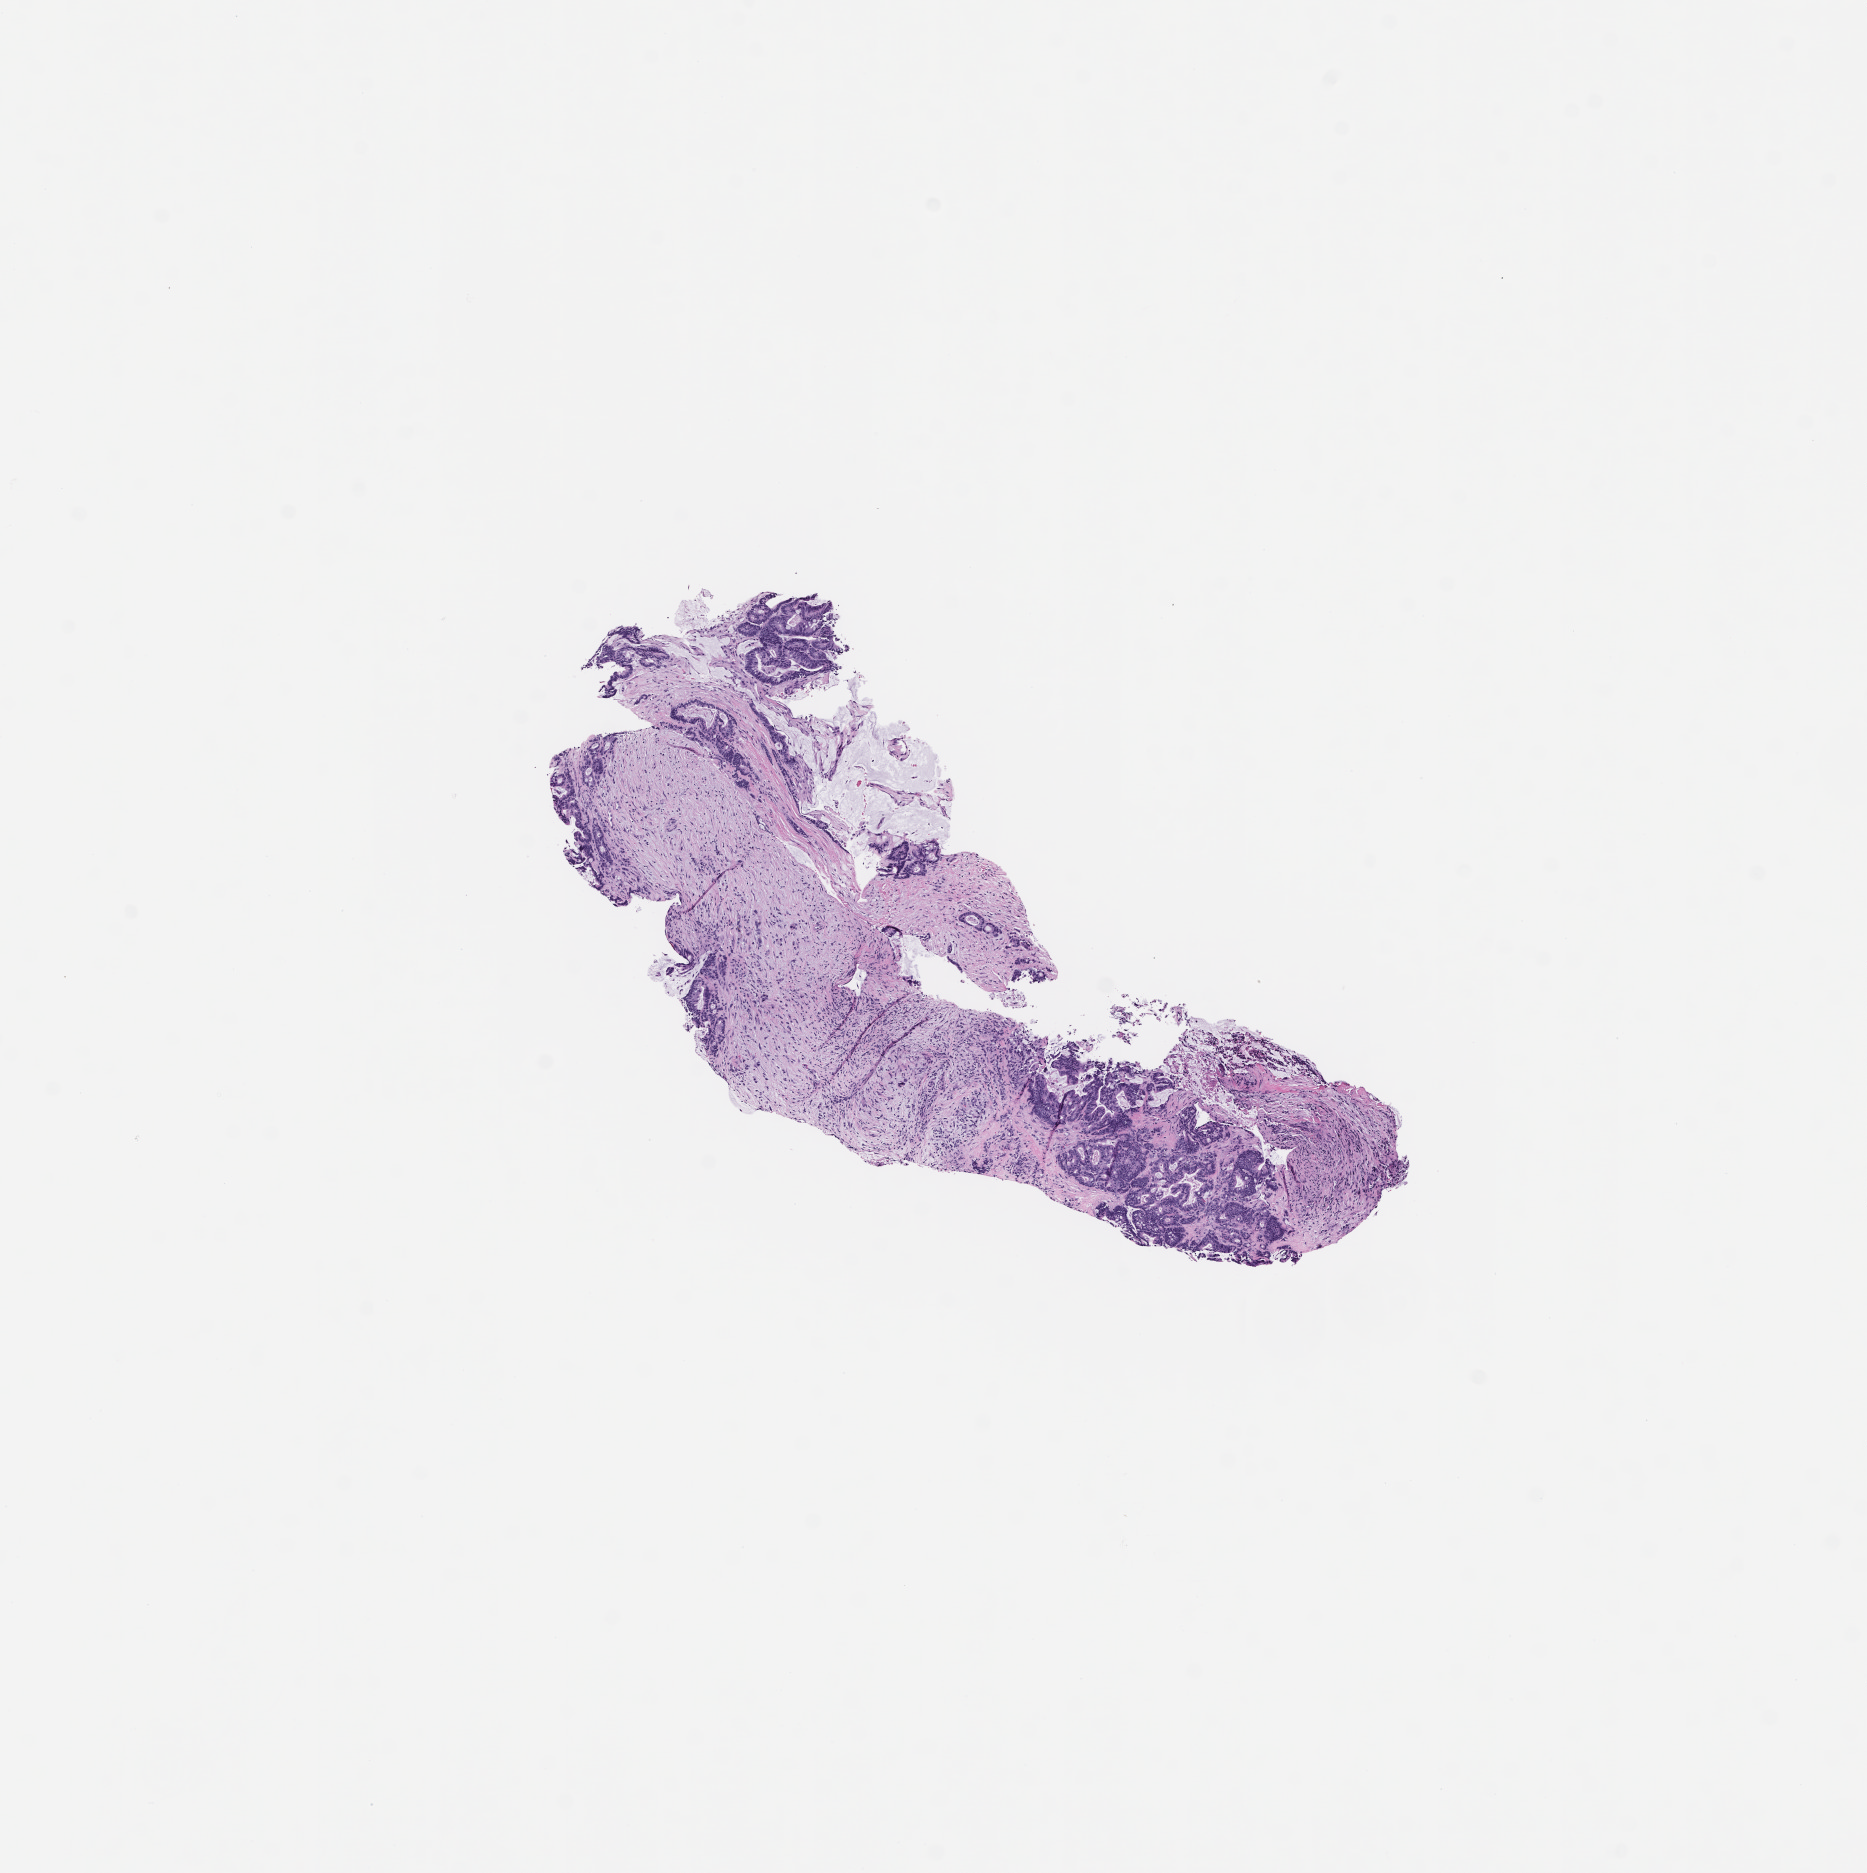
Digitized H&E-stained section, low-resolution overview of the scanned area, about 7.5 x 7.6 mm; formalin-fixed paraffin-embedded section; collected at baseline (before treatment). Patient sex: female.
This section: metastatic tumor tissue. Patient diagnosis (primary): Colorectal Carcinoma.